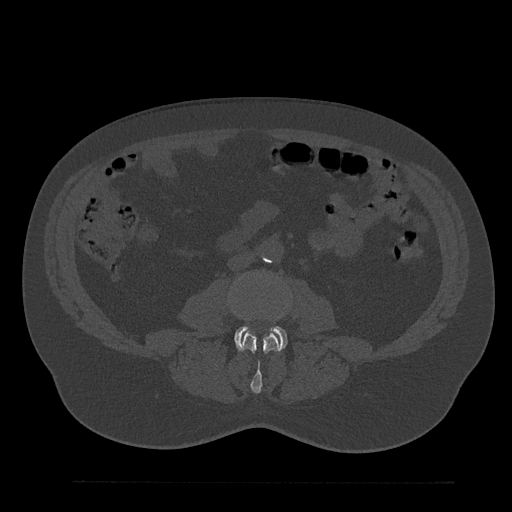
CT including the spine, one axial slice; position 1 of 797 along the scan axis; reconstruction kernel Br40s/3; 120 kVp; bone window (W 1800 / L 400 HU); 0.5 mm slice thickness; 512 × 512 image matrix, field of view 430 × 430 mm. Male patient, age 61 years. From the clinical record (not read from this slice): primary cancer: prostate.
Structures marked on this image (semi-automatic segmentation, software-assisted and operator-edited):
- L3 vertebra: bounding box [x1, y1, x2, y2] px = [231, 309, 279, 393]
- L4 vertebra: [235, 326, 287, 351]